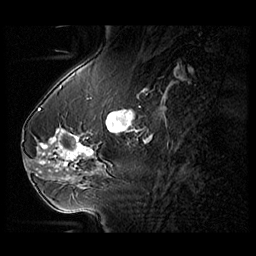
Breast MRI (dynamic contrast-enhanced), one sagittal slice; position 38 of 104 along the scan axis; 3 images stored at this slice position (order not interpretable as contrast timing); 1.5 T; TE 1.3 ms, TR 5.5 ms; 3 mm slice thickness; 256 × 256 image matrix, field of view 220 × 220 mm. Patient: female, 54 years. Case-level facts recorded for this patient, not image findings: setting: breast cancer imaged before/during neoadjuvant chemotherapy; receptor status: HR-positive, HER2-negative.
Structures marked on this image (semi-automatic segmentation, software-assisted and operator-edited):
- analysis volume of interest (the breast-tissue region the enhancement analysis was run in; not a lesion): bounding box <28,127,104,182> (left, top, right, bottom; pixels)
- tumour enhancement mask (voxels above the 140 % enhancement threshold inside the analysis volume of interest): <40,136,93,171>